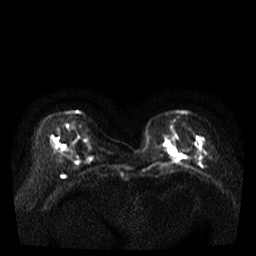
Breast MRI, one axial slice; slice 9 of 35 in the series (ordered by position); diffusion-weighted series; image 2 of 4 stored at this slice position (different b-values; order by instance number); 3 T; 256 × 256 image matrix, field of view 320 × 320 mm. Female patient.
Outlined on this slice (outlined manually by an expert reader):
- tumour on diffusion-weighted imaging: bounding box (x1, y1, x2, y2) in pixels: (169, 151, 185, 162)